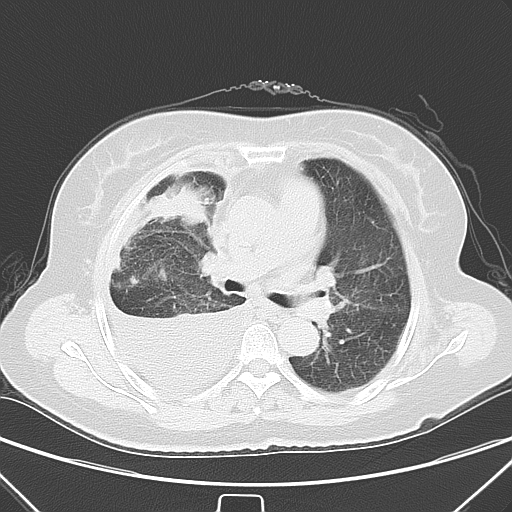
Chest CT, one axial slice; slice 36 of 55 in the series (ordered by position); lung window (W 1500 / L -600 HU); 512 × 512 image matrix. Patient: female, 66 years. Case-level facts recorded for this patient, not image findings: clinical TNM (as recorded): T2 N0 M1.
Structures marked on this image (bounding box drawn by a radiologist):
- lung tumour (recorded histology: adenocarcinoma): box from (x=145, y=186) to (x=204, y=230) px